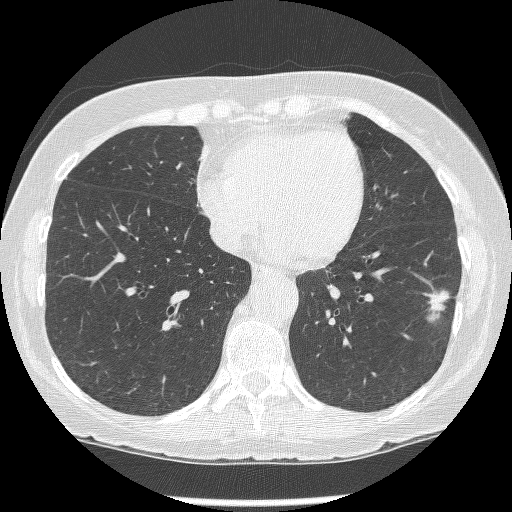
Low-dose screening chest CT, axial slice; baseline screening round; lung window (W 1500 / L -600 HU); 1.25 mm slice thickness; slice 87 of 247 in the series; 512 × 512 image matrix. Female, age 62 years at enrolment. Former smoker at enrolment.
Expert reader's lesion annotation, bounding box <421,282,462,327> (left, top, right, bottom; pixels). The screening reader recorded 2 non-calcified nodules or masses ≥4 mm on this exam (left lower lobe, left lower lobe); which of them this box marks is not recorded. Lung cancer was diagnosed 15 days after this screen: non-small cell carcinoma, left lower lobe, stage IIIB (AJCC 6th edition), 23 mm at pathology.